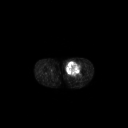
FDG PET of an extremity soft-tissue mass (from a PET/CT study), one axial slice. Slice 237 of 267 in the series (ordered by position). 3.27 mm slice thickness. 128 × 128 image matrix, field of view 700 × 700 mm. Patient: male, 63 years. From the clinical record (not read from this slice): histological type: pleiomorphic liposarcoma; grade: high; site of the primary tumour: left thigh.
Annotated regions visible in this slice (expert contour drawn on MRI and transferred to this co-registered scan by the dataset authors):
- gross tumour volume including surrounding oedema: bounding box <66,61,82,76> (left, top, right, bottom; pixels)
- gross tumour volume (mass): <66,61,80,76>